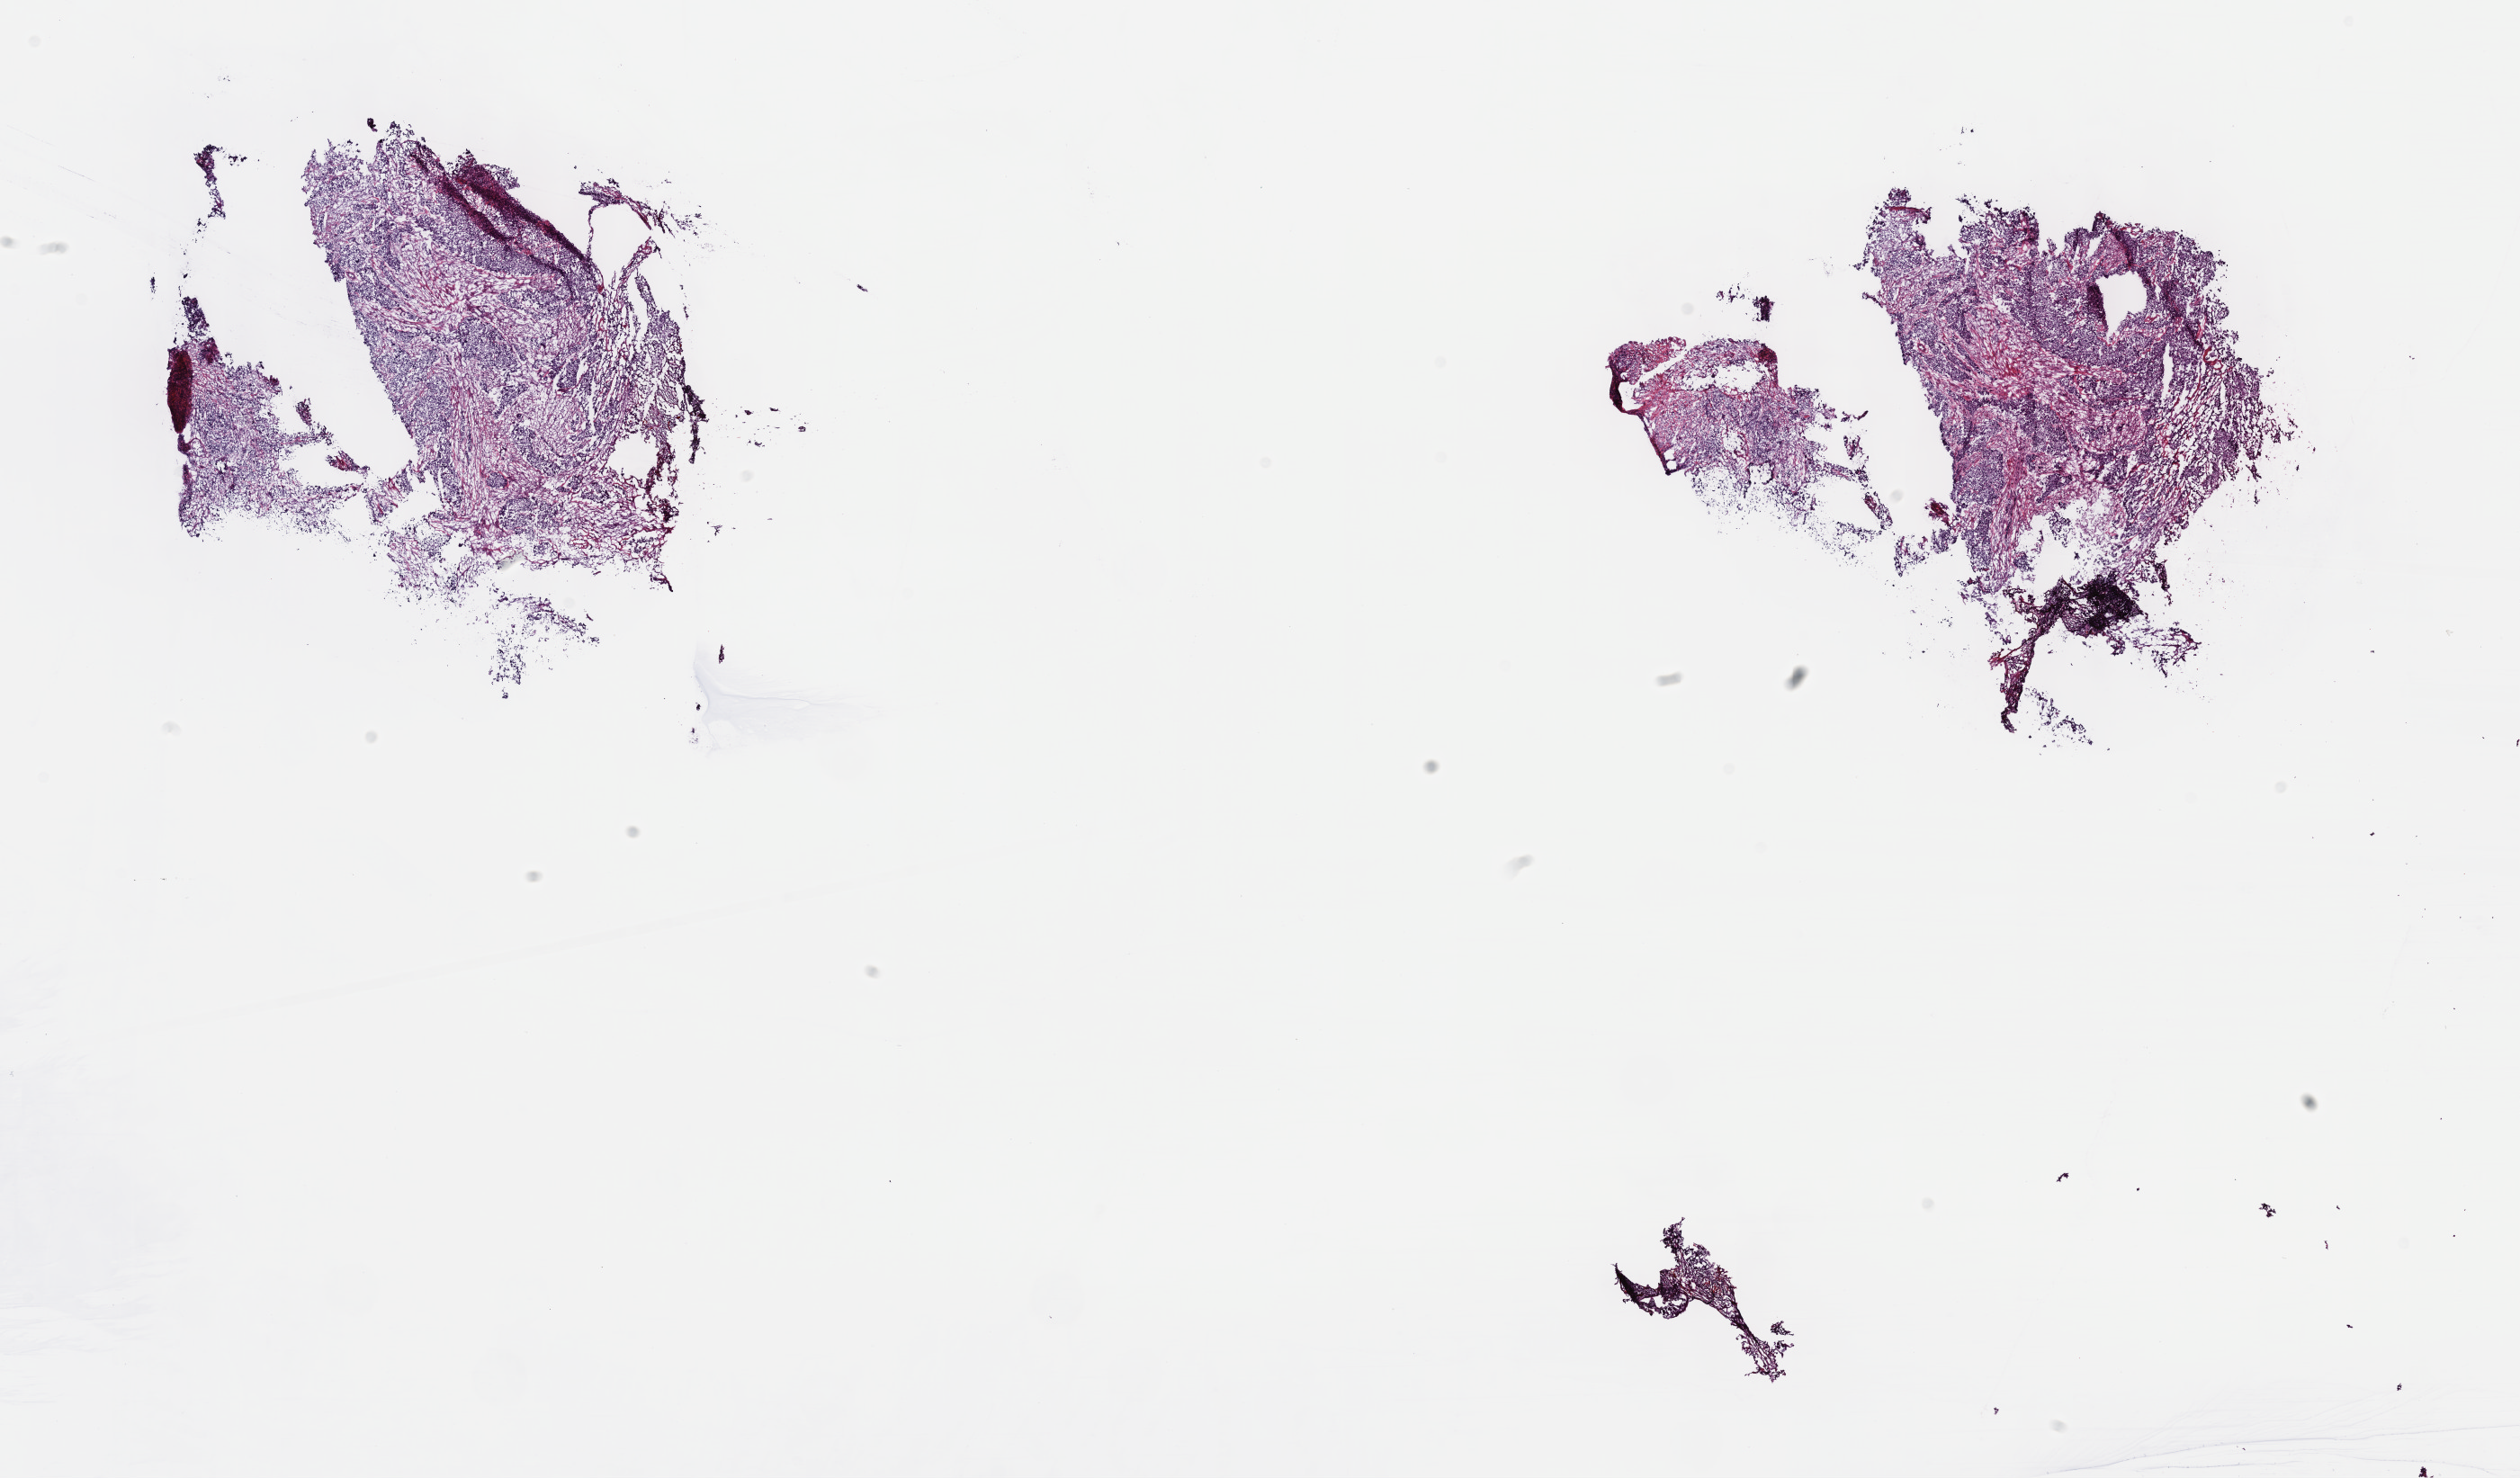
Whole-slide histology image, H&E, low-resolution overview of the scanned area, about 22.7 x 13.3 mm (from a 40x scan). Frozen section from the top of the tissue portion. Primary tumour sample from the bladder. Patient: male, age at initial diagnosis 80 years. Pathologist review of this section (percent, as recorded): tumour cells 50%, tumour nuclei 60%.
Diagnosis: Transitional cell carcinoma.